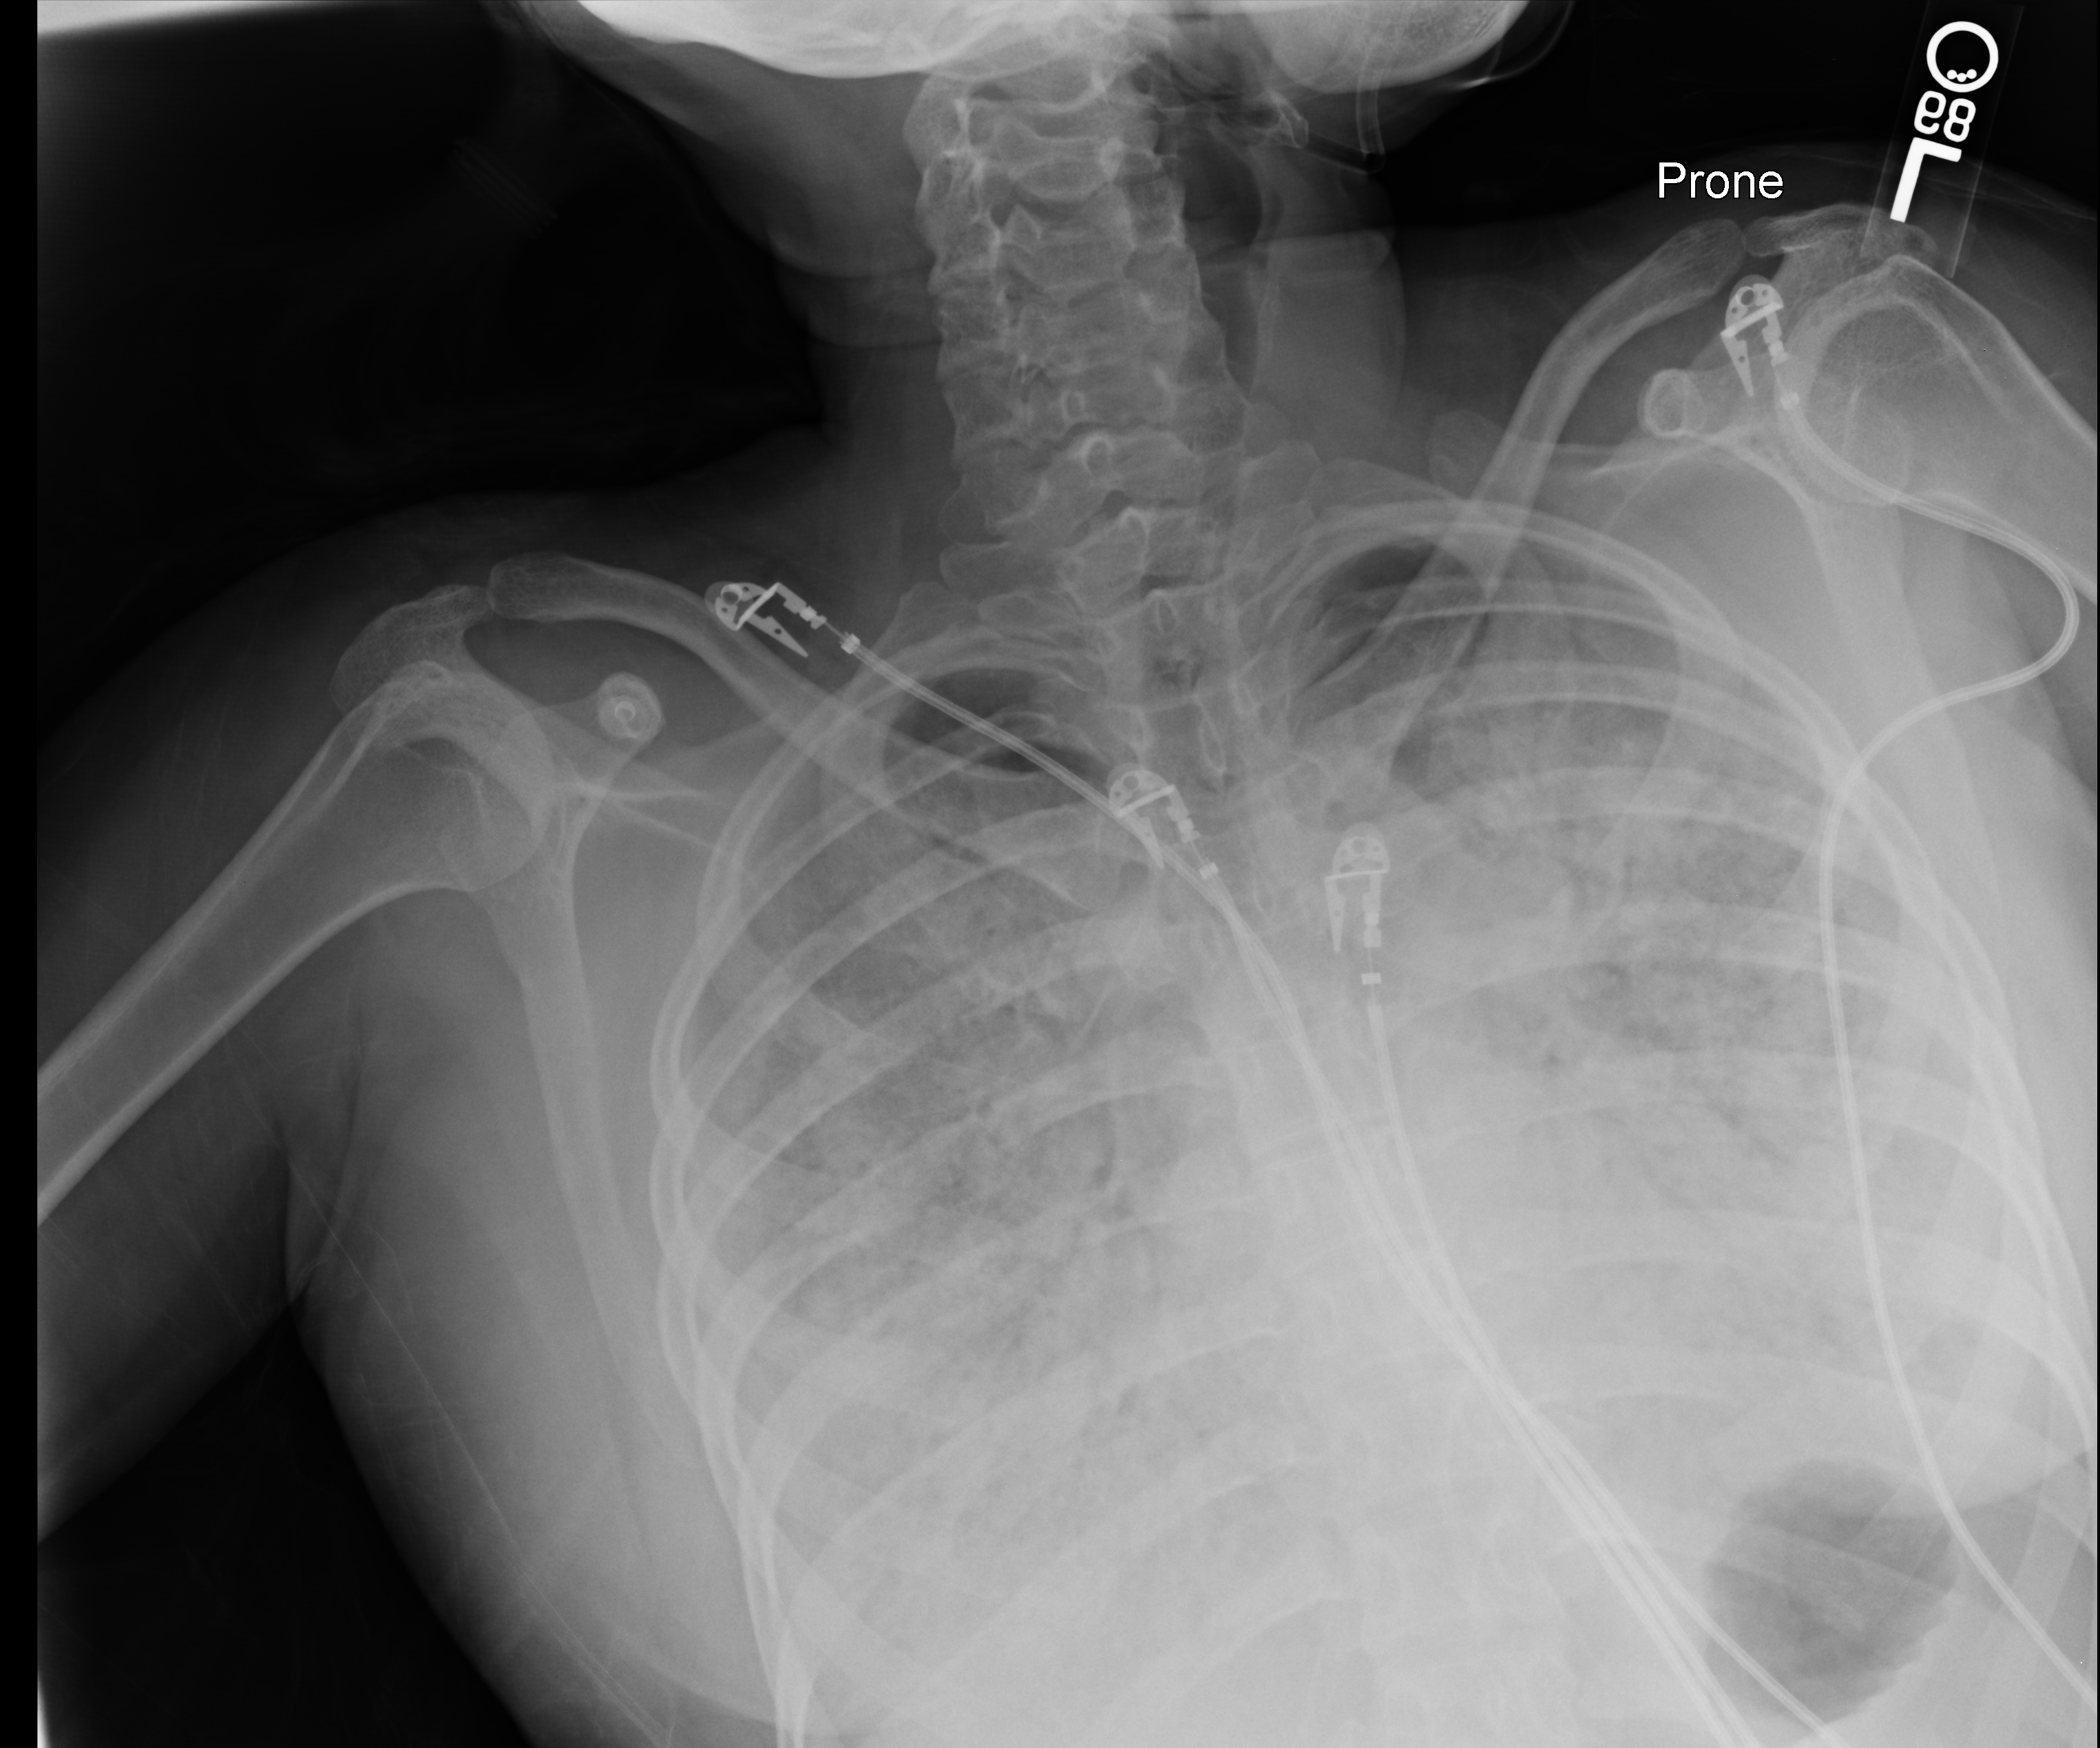
Bedside chest radiograph (computed radiography), anteroposterior (AP) projection. Patient hospitalised with COVID-19, aged 18–59 years.
From the hospital-stay record, not from the radiograph (when in the stay this image was taken is not recorded): admitted to intensive care during this hospital stay: yes; chronic kidney disease (admission record): no; length of hospital stay: 30 days.